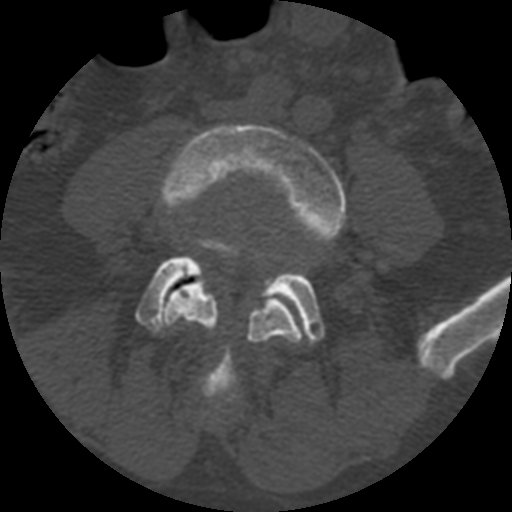
CT including the spine, one axial slice. Slice 269 of 399 in the series (ordered by position). Bone window (W 1800 / L 400 HU). 1.25 mm slice thickness. 512 × 512 image matrix, field of view 160 × 160 mm. Patient age 71 years. From the clinical record (not read from this slice): primary cancer: prostate.
Annotated regions visible in this slice (semi-automatic segmentation, software-assisted and operator-edited):
- L4 vertebra: box from (x=159, y=125) to (x=346, y=406) px
- L5 vertebra: (x=136, y=239)–(x=326, y=406)